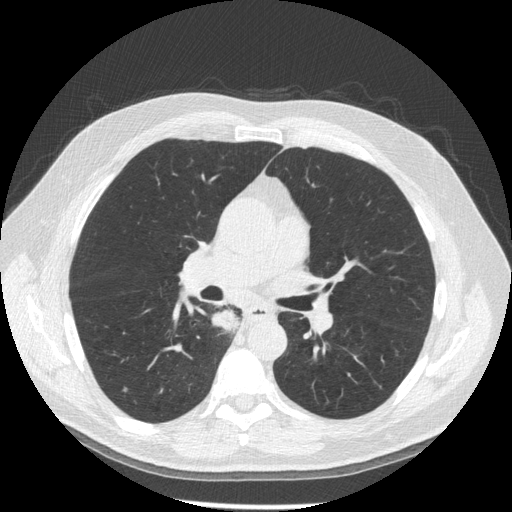
Axial slice from a low-dose chest CT screening exam, third screening round (two years after baseline), lung window (W 1500 / L -600 HU), slice 78 of 181 in the series, 512 × 512 image matrix, field of view 370 × 370 mm. Male, age 61 years at enrolment.
• Expert-annotated lung lesion, box from (x=207, y=299) to (x=255, y=345) px.
• Screening reader's record for this exam: no non-calcified nodule ≥4 mm recorded.